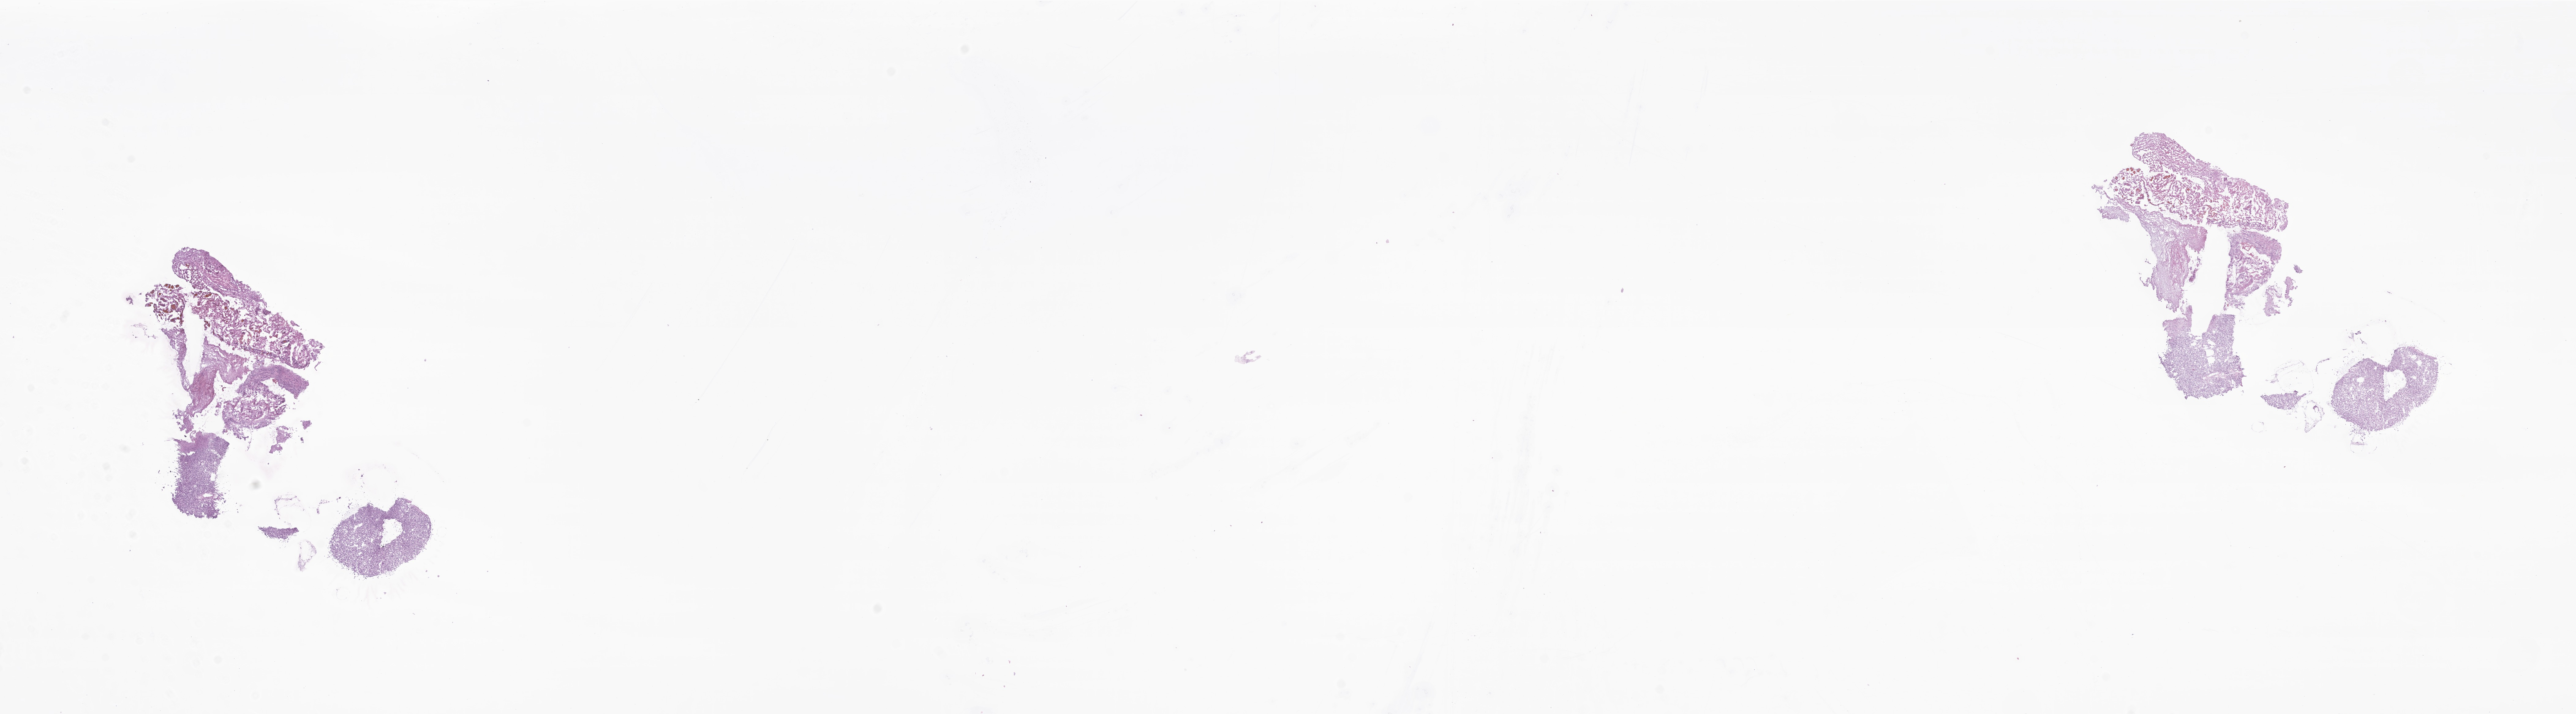
Haematoxylin and eosin whole-slide image of tumor tissue from the cerebellum — whole scanned area (about 35.5 x 9.8 mm) shown as a low-resolution overview, cryosection (OCT / tissue freezing medium). Patient female; age 196 months (16 years 4 months).
Recorded diagnosis: Hemangioblastoma.